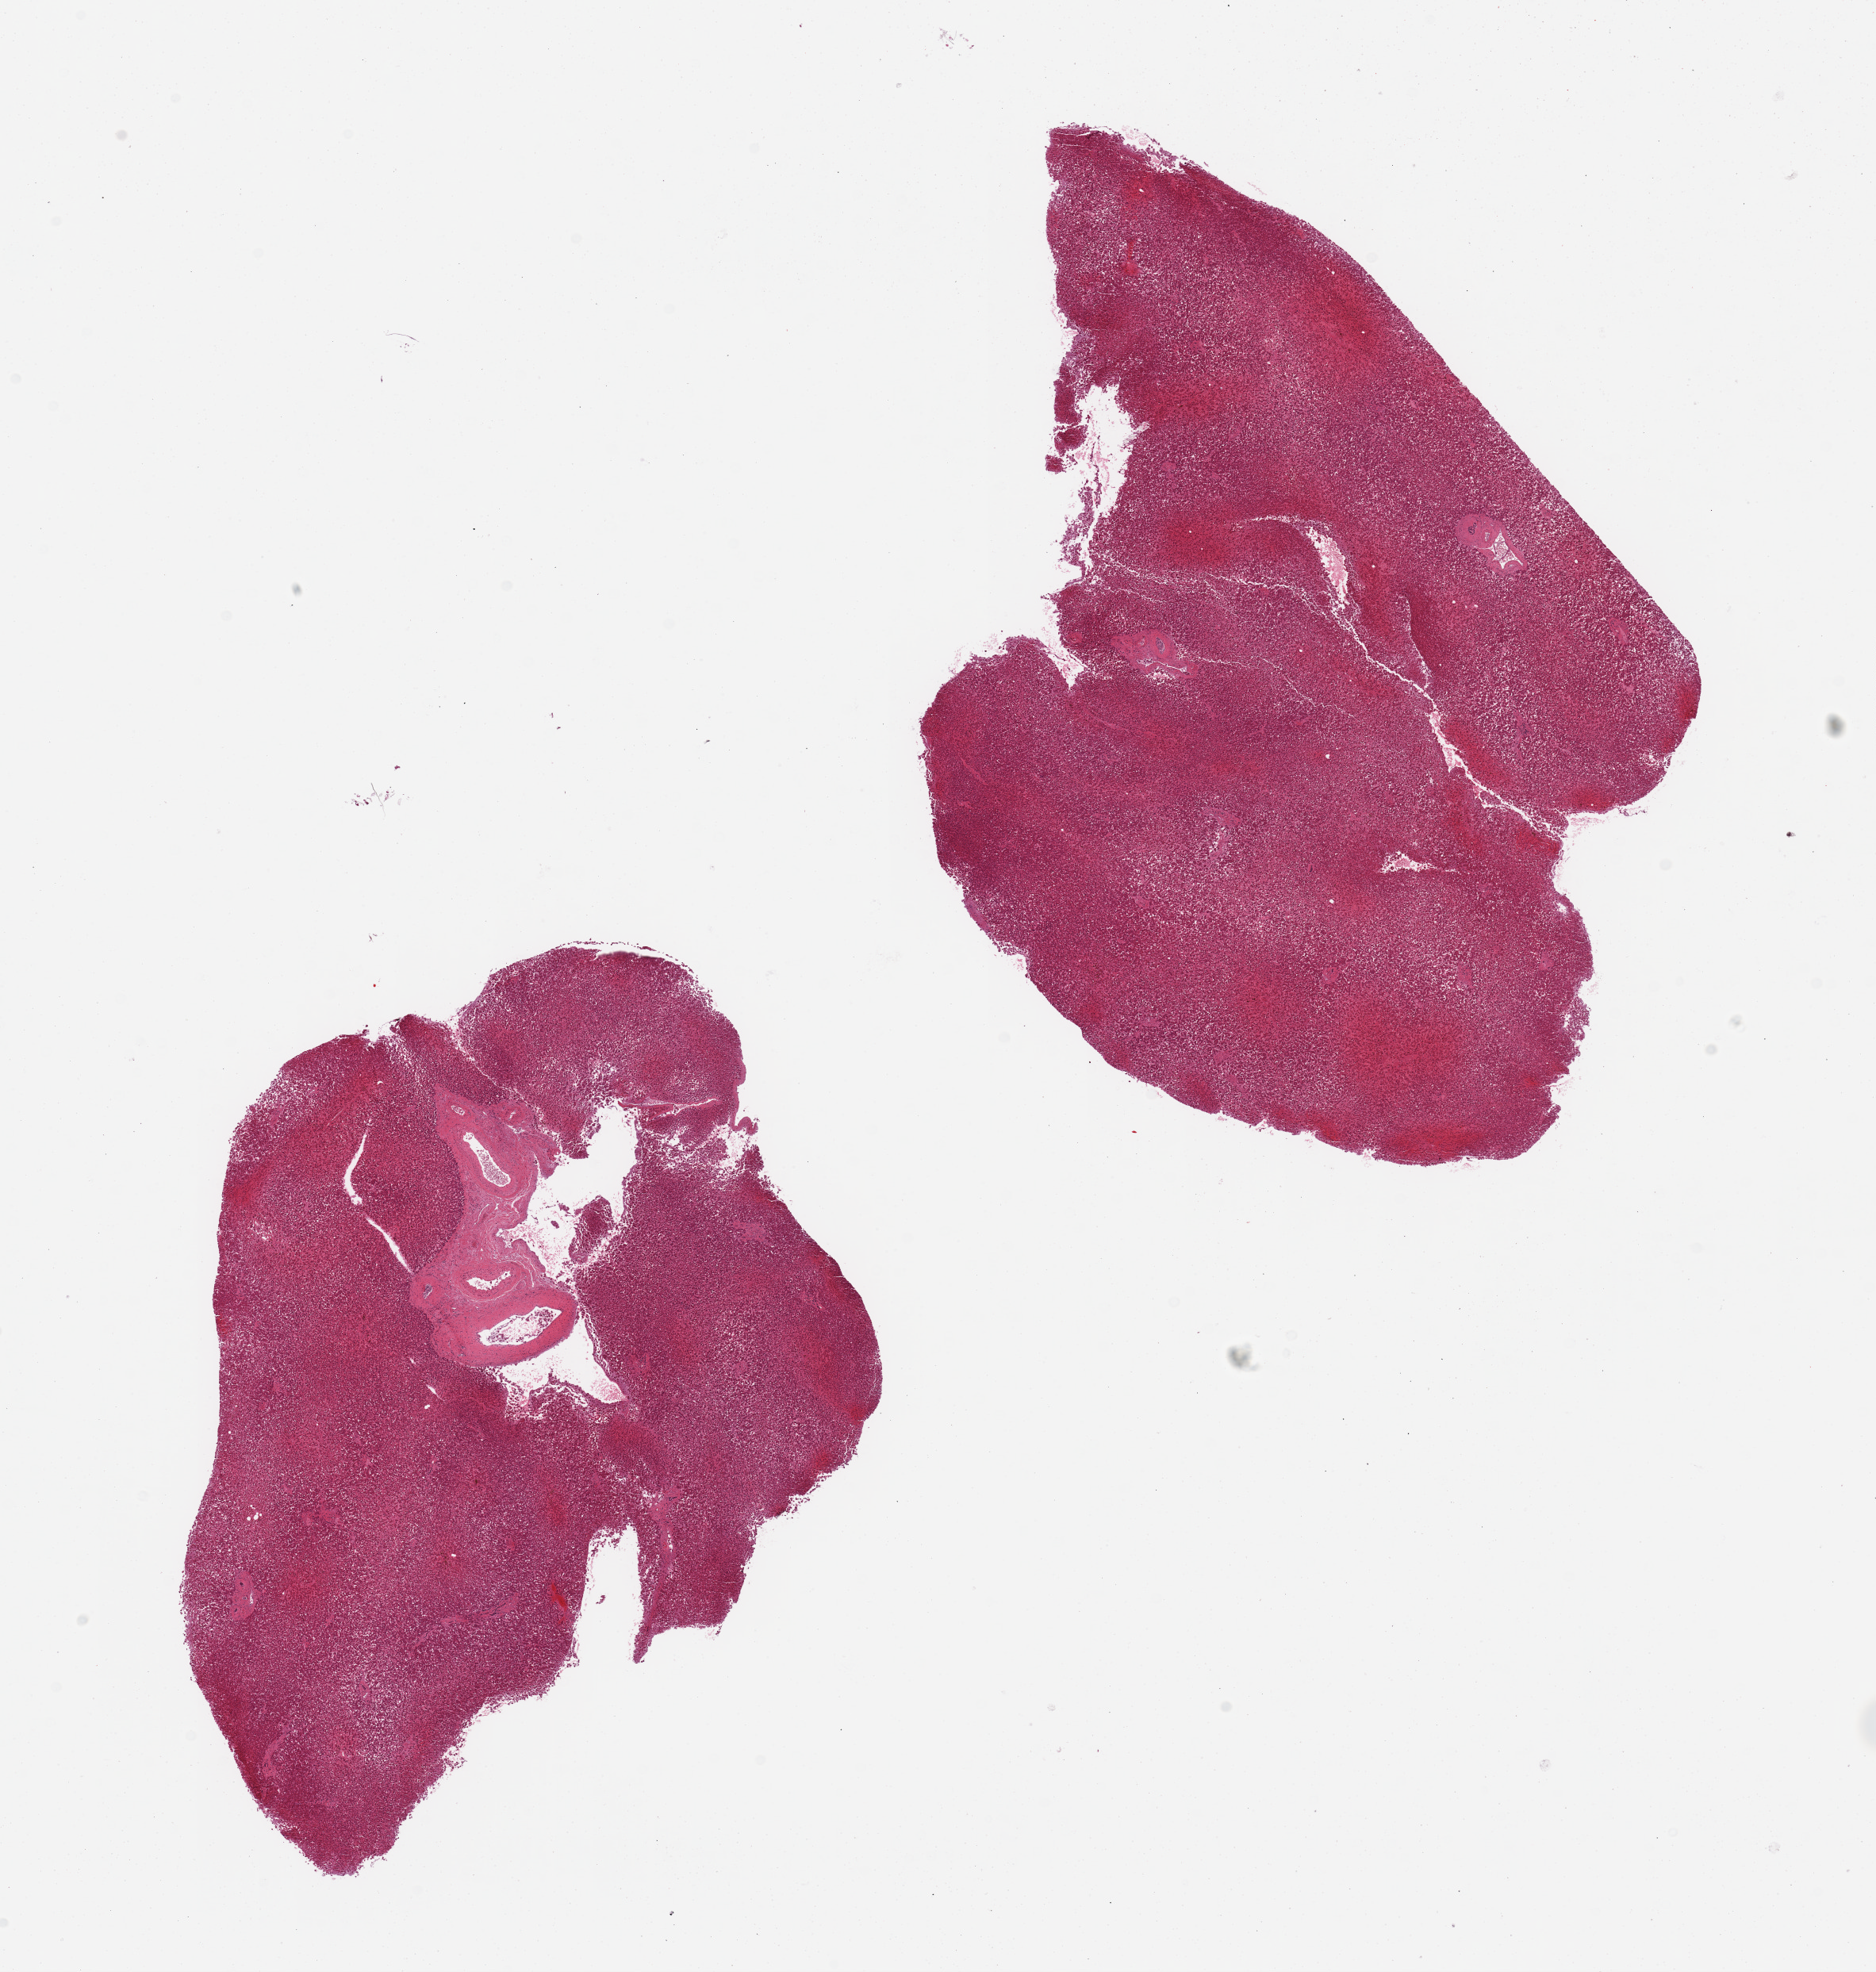
Digitized haematoxylin and eosin-stained section — whole scanned area (about 18.7 x 19.7 mm, acquisition: 20x scan) shown as a low-resolution overview; PAXgene-fixed, paraffin-embedded tissue; sampled site (target tissue): liver; tissue donor sample. Donor sex: female.
Pathologist's review note for this sample: 2 pieces, congested.